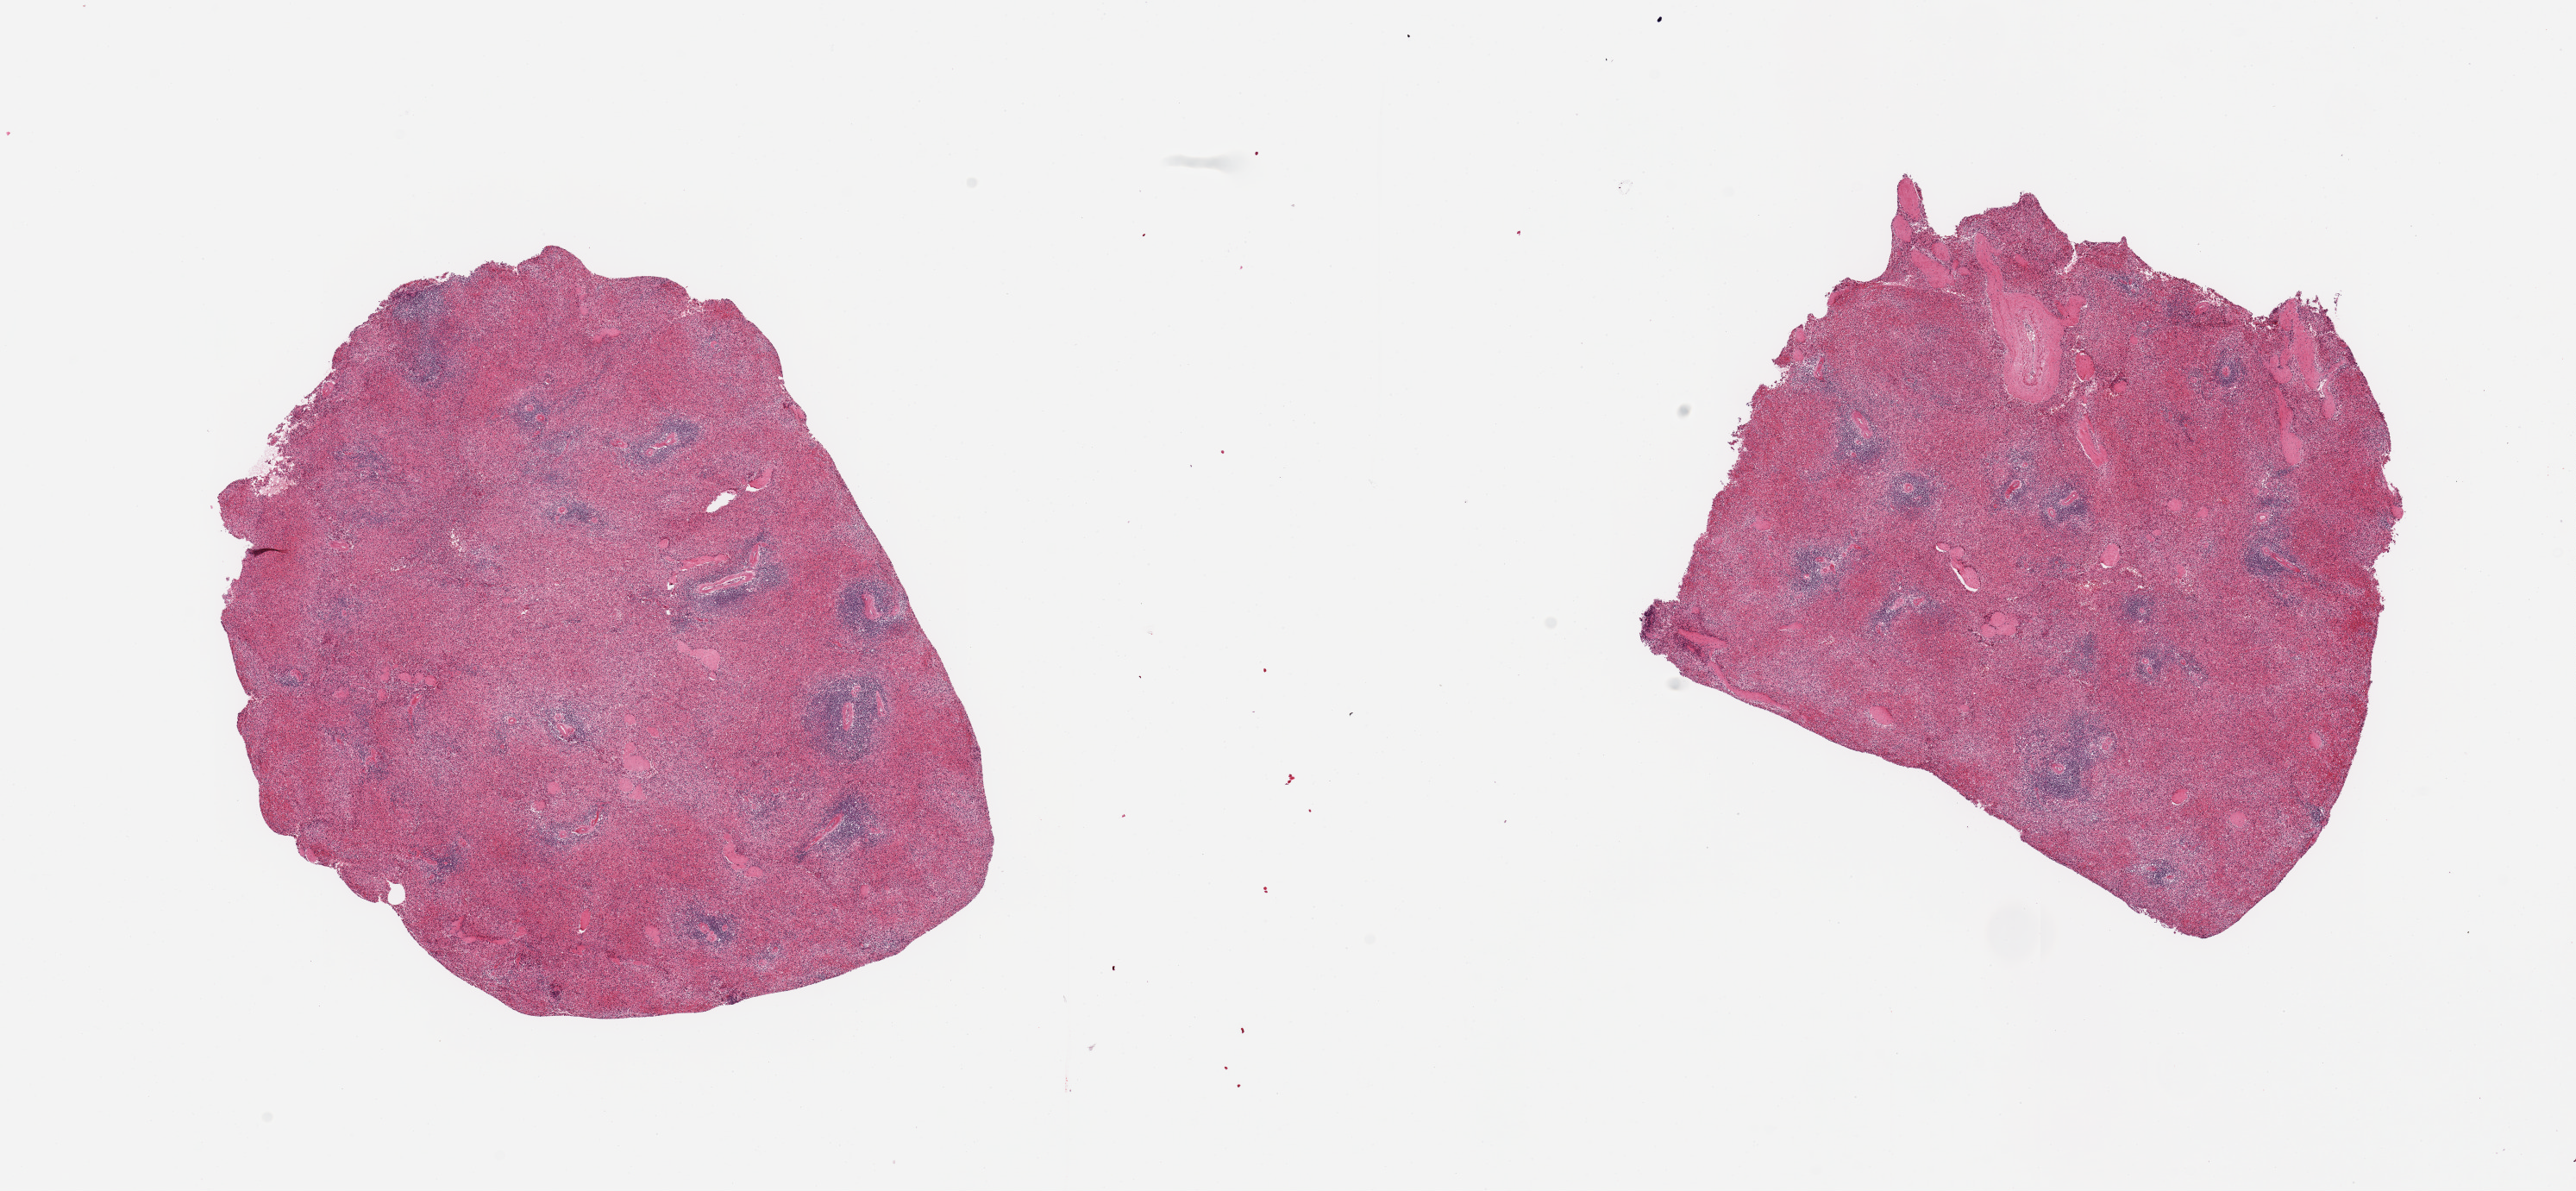
Whole-slide image, hematoxylin and eosin (H&E) stain, whole scanned area (about 23.6 x 10.9 mm) shown as a low-resolution overview, PAXgene-fixed, paraffin-embedded tissue, section of spleen (target tissue), donor tissue sample.
Review note (as recorded): 2 pieces, no abnormalities.